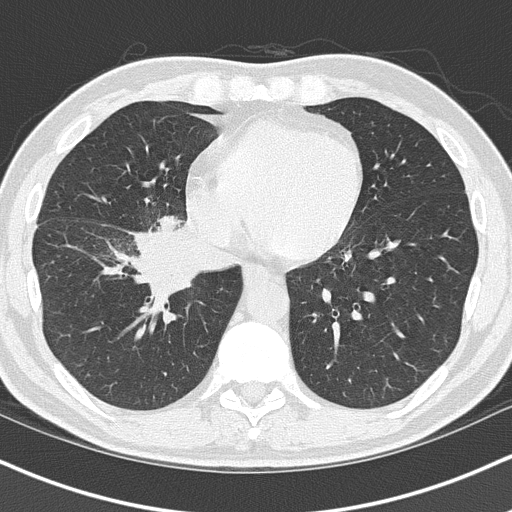
Low-dose screening chest CT, axial slice. First (baseline) screen. Lung window (W 1500 / L -600 HU). 2 mm slice thickness. Lung (sharp) reconstruction kernel (B50f). Slice 47 of 151 in the series. 512 × 512 image matrix. Male, age 55 years at enrolment. Current smoker at enrolment.
Expert reader's lesion annotation, bounding box <127,224,242,311> (left, top, right, bottom; pixels). Screening reader's record for this exam (one nodule recorded; not confirmed to be the boxed lesion): non-calcified nodule or mass ≥4 mm, right lower lobe, 6 × 5 mm, spiculated (stellate) margins, soft tissue attenuation. Official screen result: positive, change unspecified: nodule(s) >= 4 mm or enlarging nodule(s), mass(es), or other non-specific abnormalities suspicious for lung cancer. Participant outcome: lung cancer diagnosed 21 days after this screen — carcinoma, NOS, right hilum, stage IB (AJCC 6th edition), 67 mm at pathology.